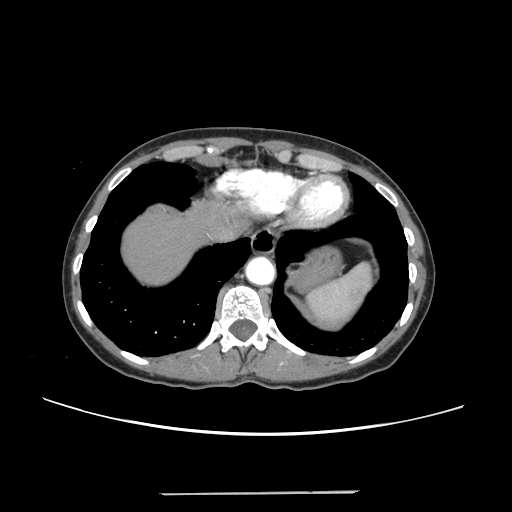
Contrast-enhanced abdominal CT, one axial slice. Intravenous contrast given. Soft-tissue window (W 400 / L 40 HU). 1.25 mm slice thickness. 512 × 512 image matrix, field of view 371 × 371 mm. Female patient, age 60 years. Case-level facts recorded for this patient, not image findings: diagnosis: colorectal cancer liver metastases, imaged before liver resection; multiple liver metastases: no; largest metastasis: 1.5 cm.
Annotated regions visible in this slice (manually delineated by an expert):
- liver: bounding box [x1, y1, x2, y2] px = [123, 203, 229, 285]
- planned liver remnant (the part of the liver to remain after resection): [123, 203, 229, 285]